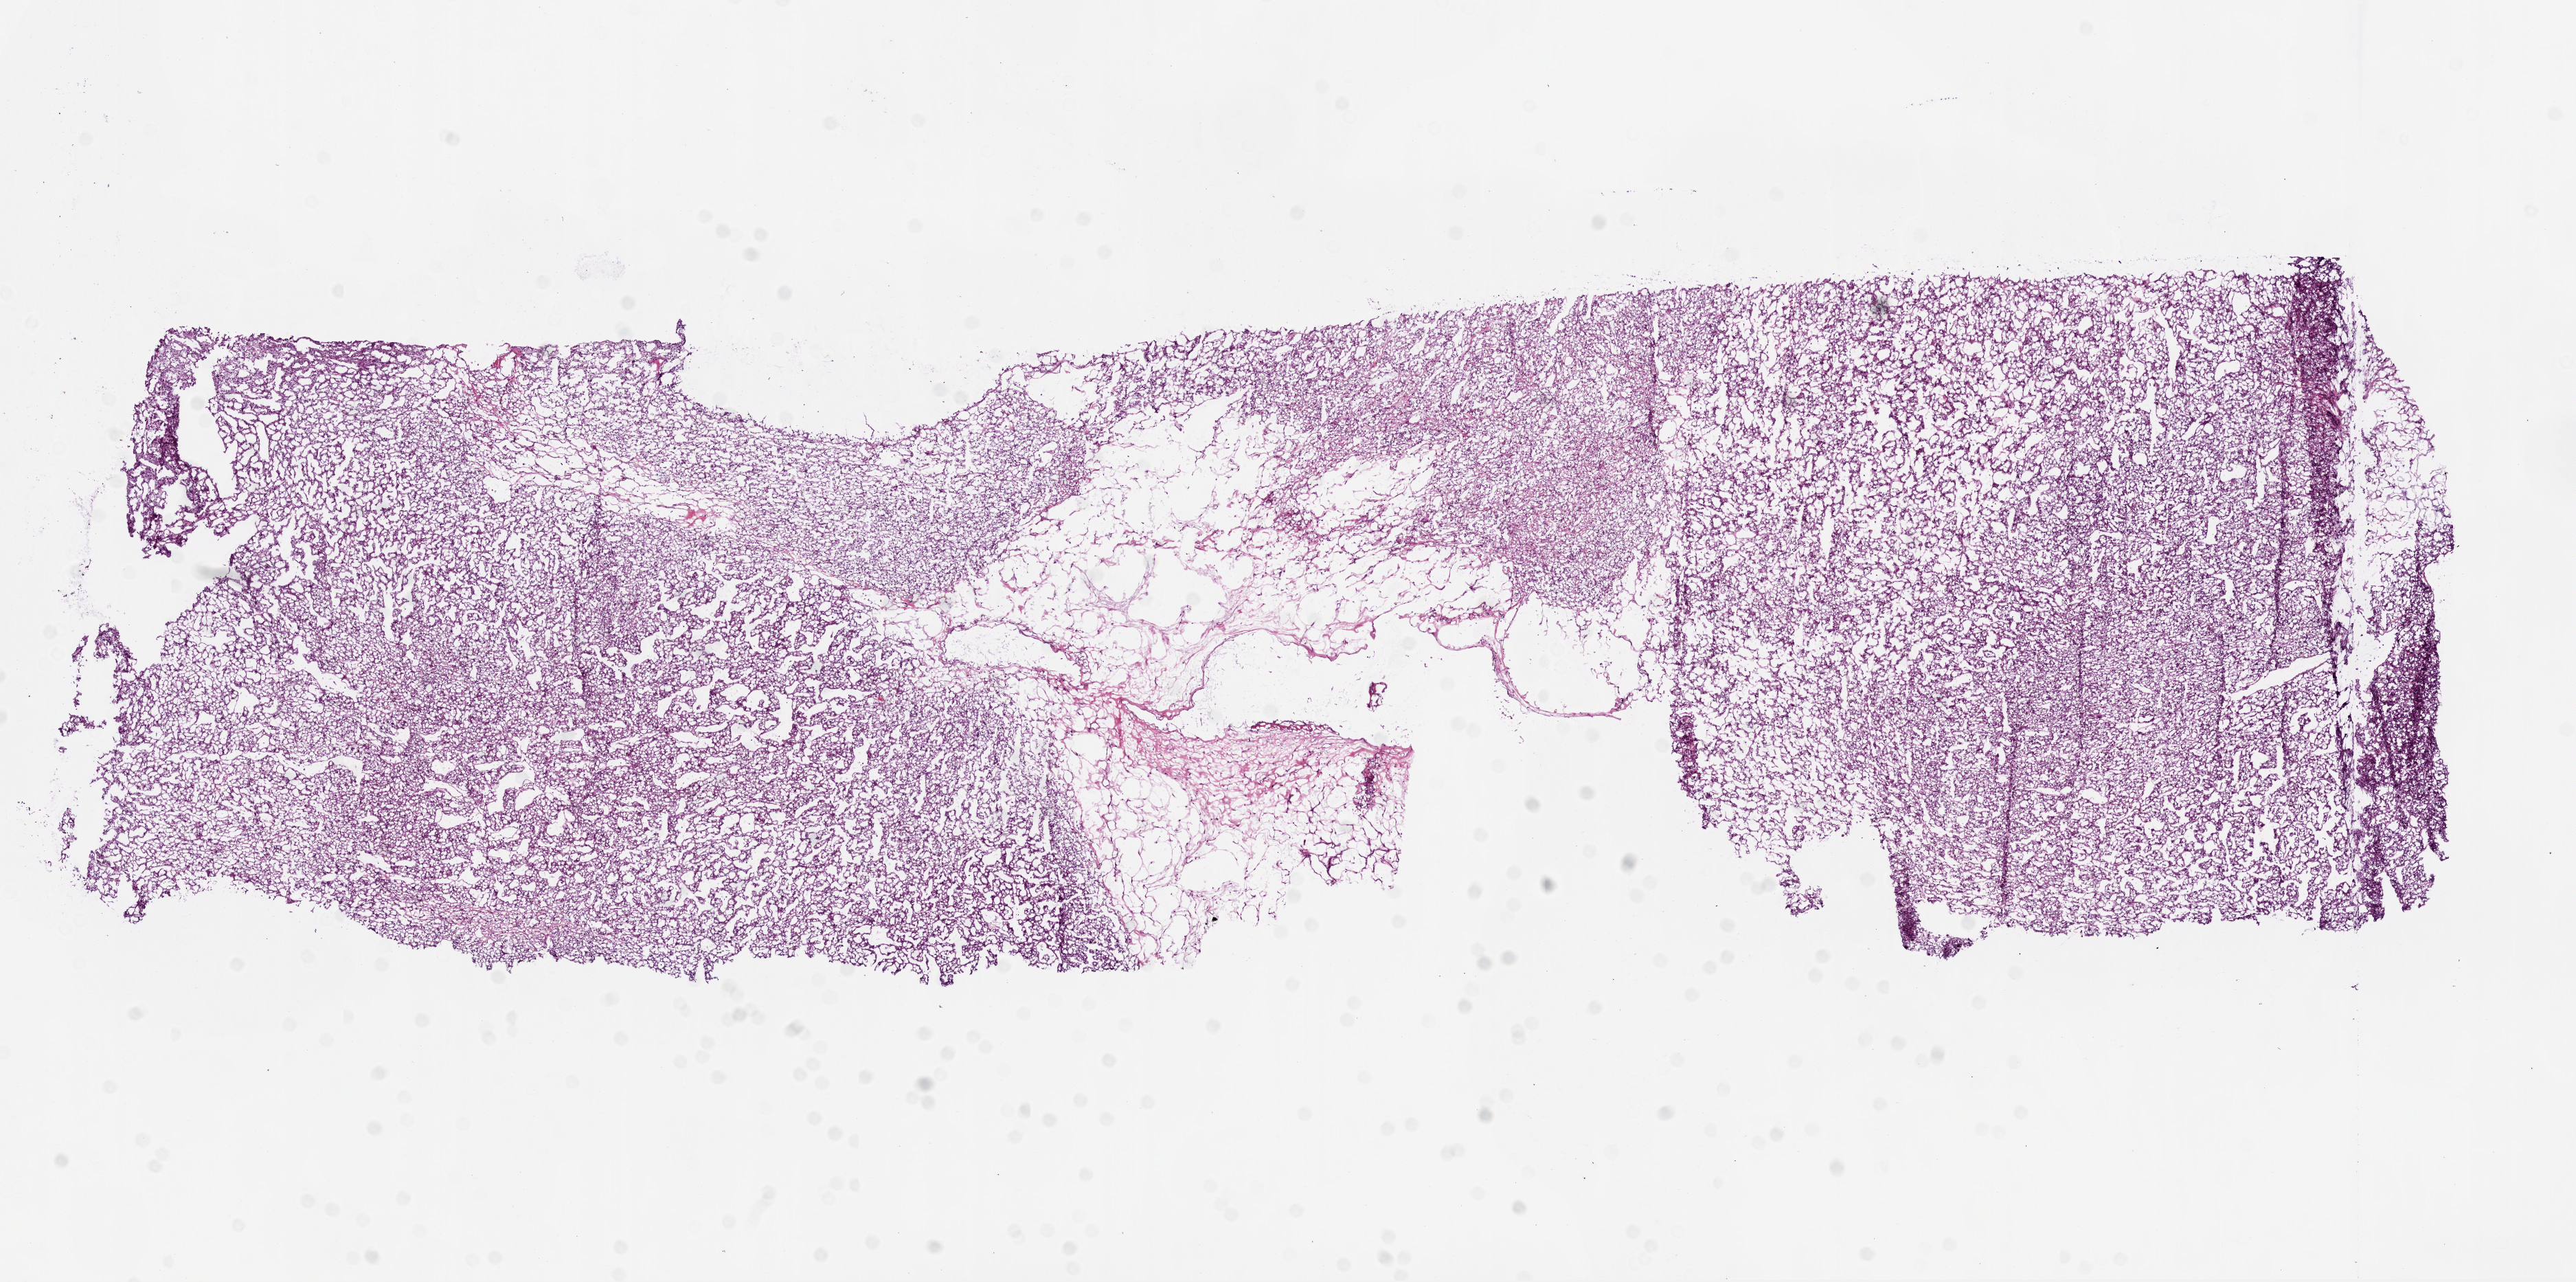
Digitized H&E-stained tissue section (whole slide), a low-resolution overview of the entire scanned area, about 15.0 x 7.5 mm. Frozen section. Primary tumour sample from the kidney. Female patient; age at initial diagnosis 68 years. Histologic grade: G3 (poorly differentiated). Composition of this section per pathologist review: tumour cells 82%, tumour nuclei 80%, normal cells 0%, stromal cells 18%, necrosis 0%.
AJCC pathologic stage: IV. Histologic diagnosis: Clear cell adenocarcinoma, NOS.